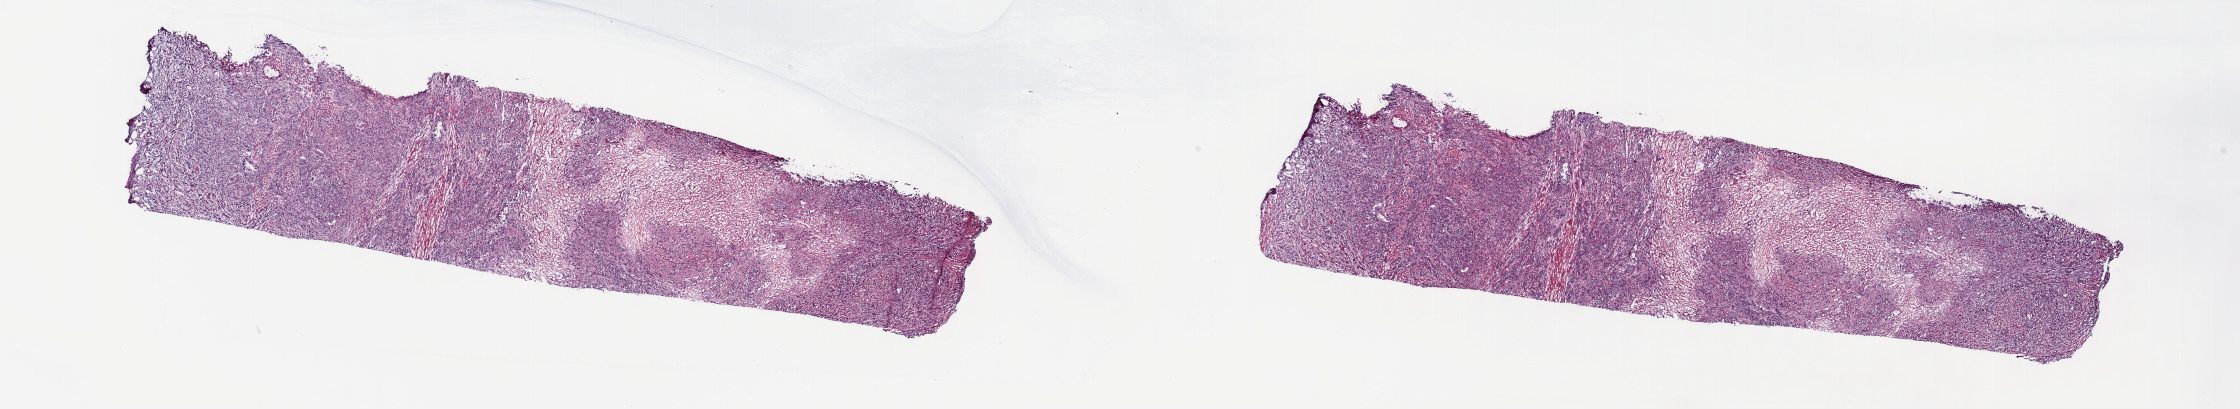
Whole-slide histology image, H&E-stained, whole scanned area (about 36.2 x 6.6 mm, from a 40x scan) shown as a low-resolution overview; frozen section from the top of the tissue portion; primary tumour sample from the bladder. Male, age 77 years at initial diagnosis. Histologic grade: high grade. Pathologist review of this section (percent, as recorded): tumour cells 81%, tumour nuclei 80%, normal cells 0%, stromal cells 0%, necrosis 19%. Infiltration values recorded for this section: lymphocyte infiltration 2%, monocyte infiltration 0%, neutrophil infiltration 0%.
• diagnosis: Transitional cell carcinoma
• lymph nodes positive (case pathology): 0 of 71 examined
• AJCC pathologic stage: III